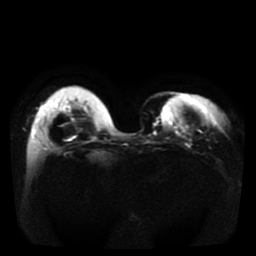
Breast MRI, one axial slice; slice 11 of 41 in the series (ordered by position); diffusion-weighted series; image 2 of 4 stored at this slice position (different b-values; order by instance number); 1.5 T; 5 mm slice thickness; 256 × 256 image matrix, field of view 330 × 330 mm. Female patient.
Annotated regions visible in this slice (expert manual segmentation):
- tumour on diffusion-weighted imaging: bounding box <179,133,182,136> (left, top, right, bottom; pixels)